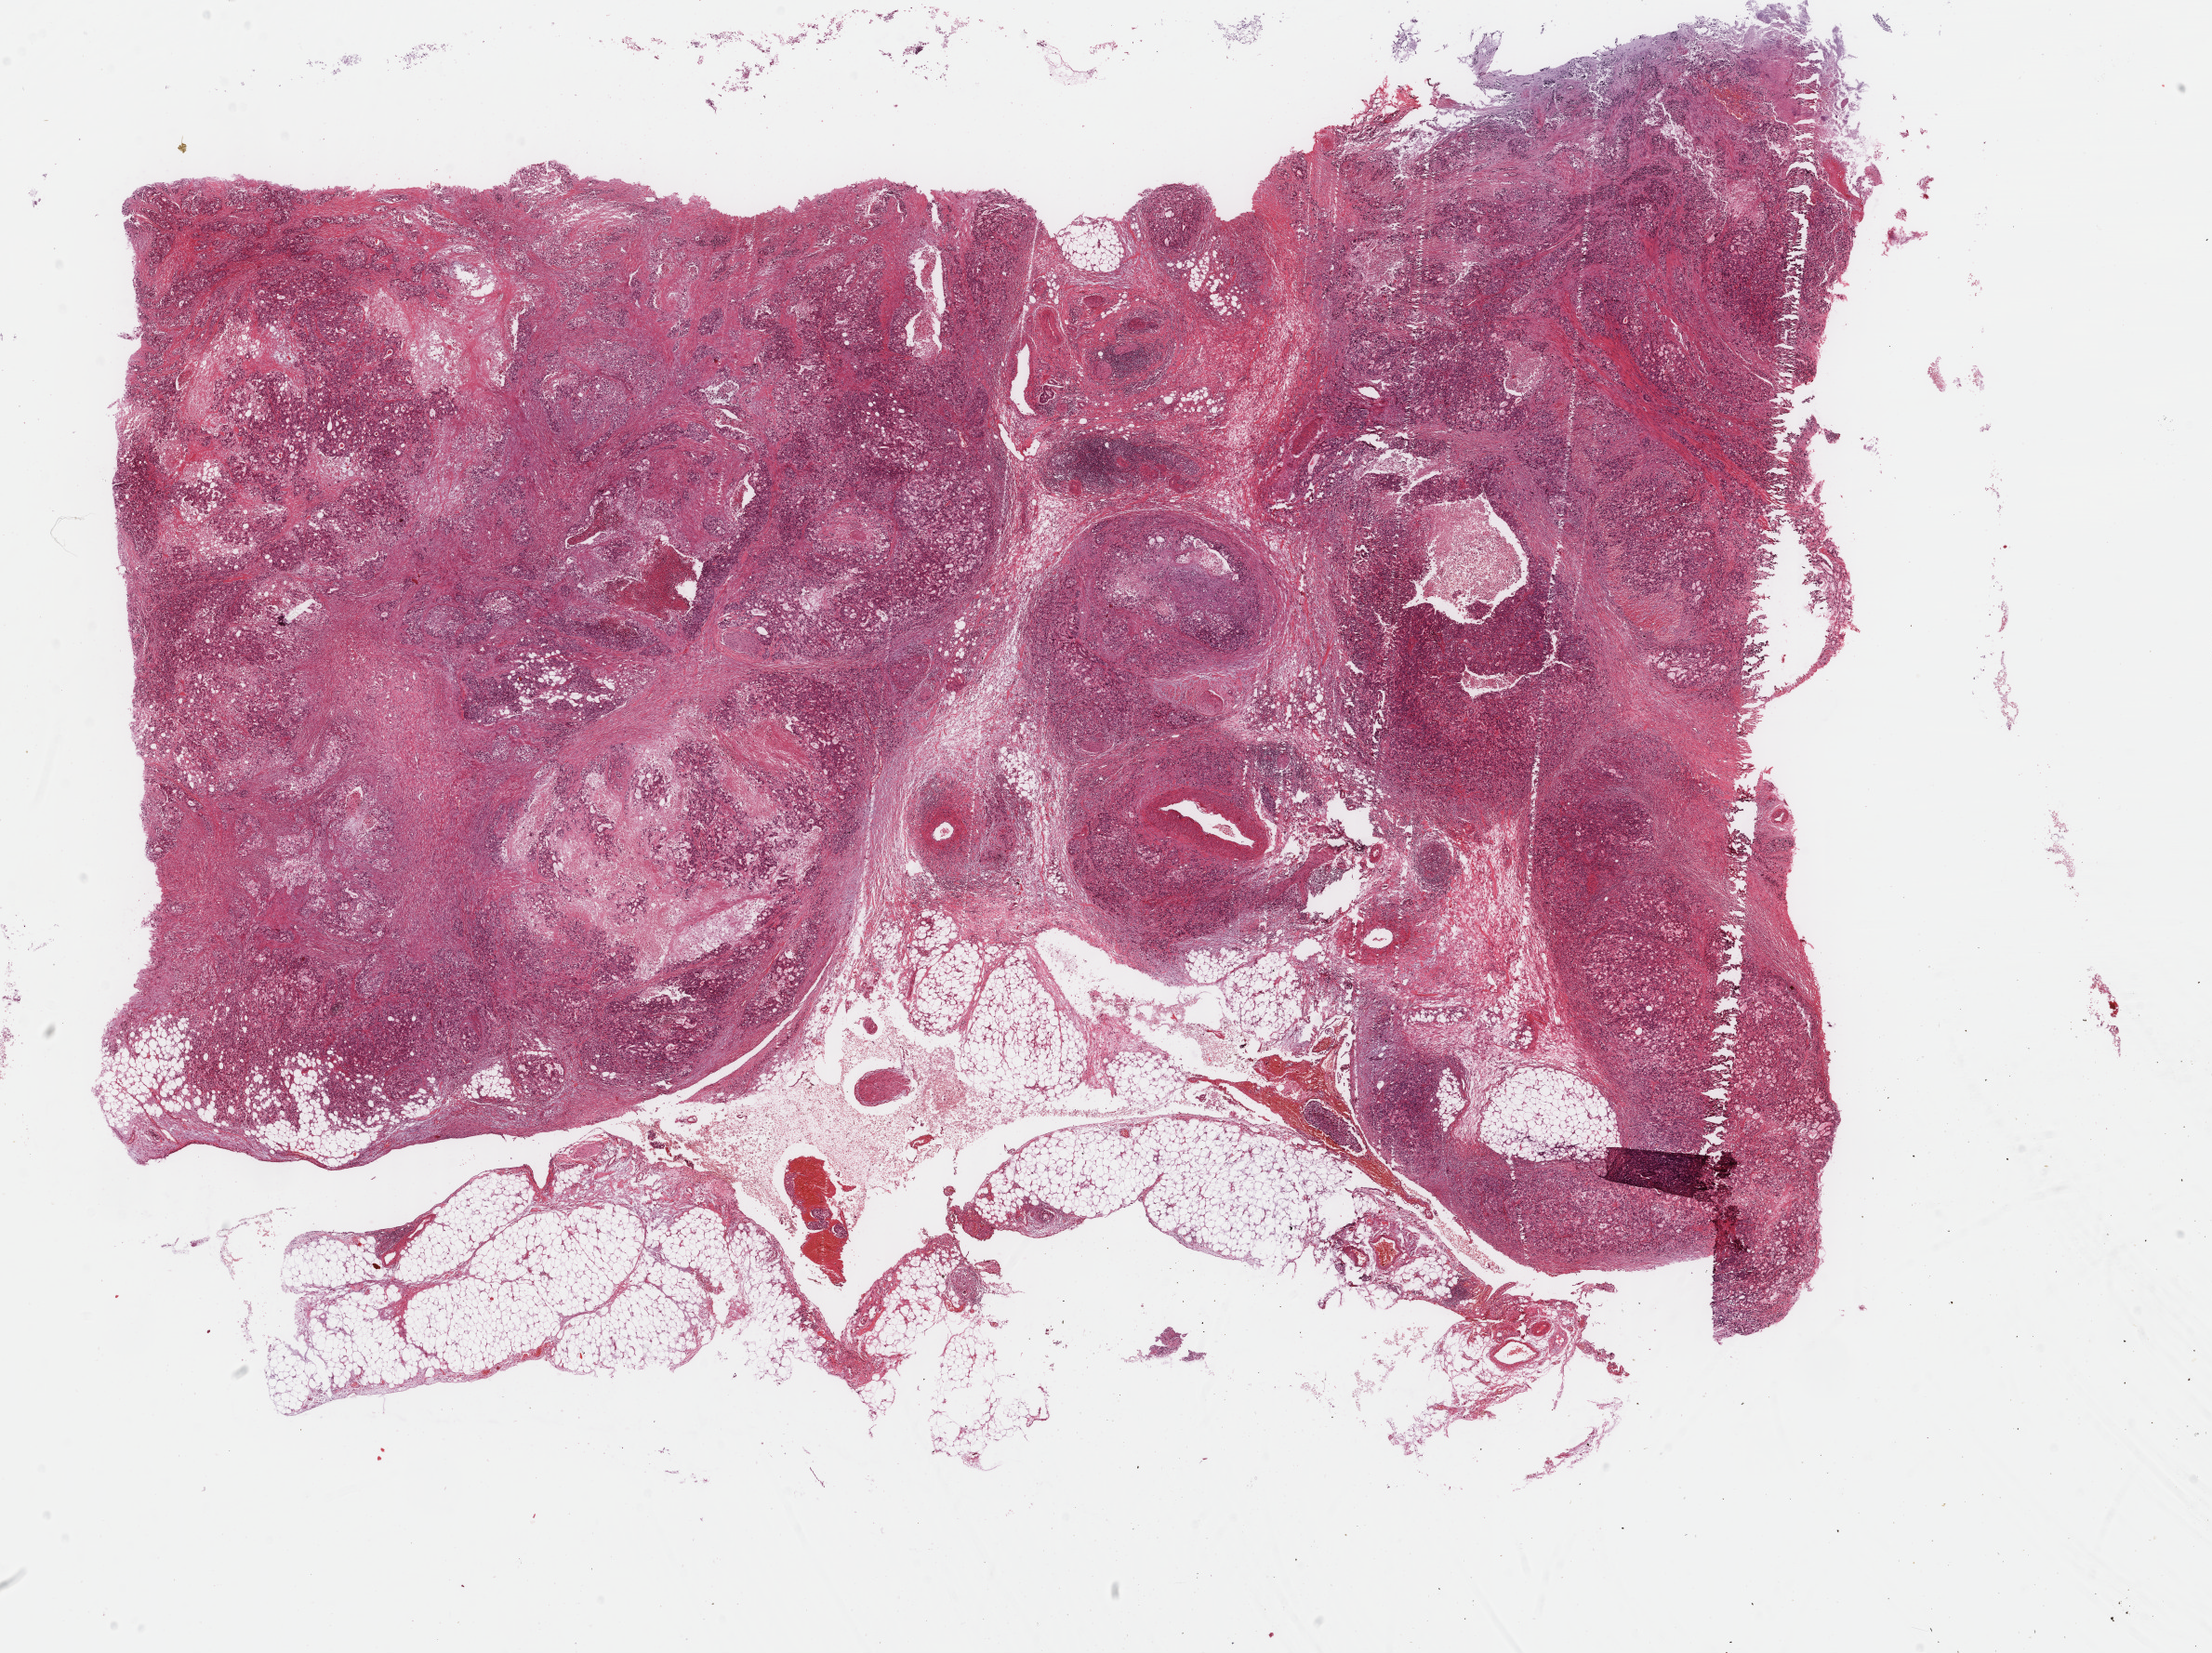
Whole-slide histology image, H&E, a low-resolution overview of the entire scanned area, about 18.9 x 14.1 mm (from a 40x scan); FFPE section; sample: primary tumour, stomach. Female patient; age at initial diagnosis 79 years. Histologic grade: G3 (poorly differentiated).
- AJCC pathologic stage: IIB
- pathologic diagnosis: Adenocarcinoma, NOS